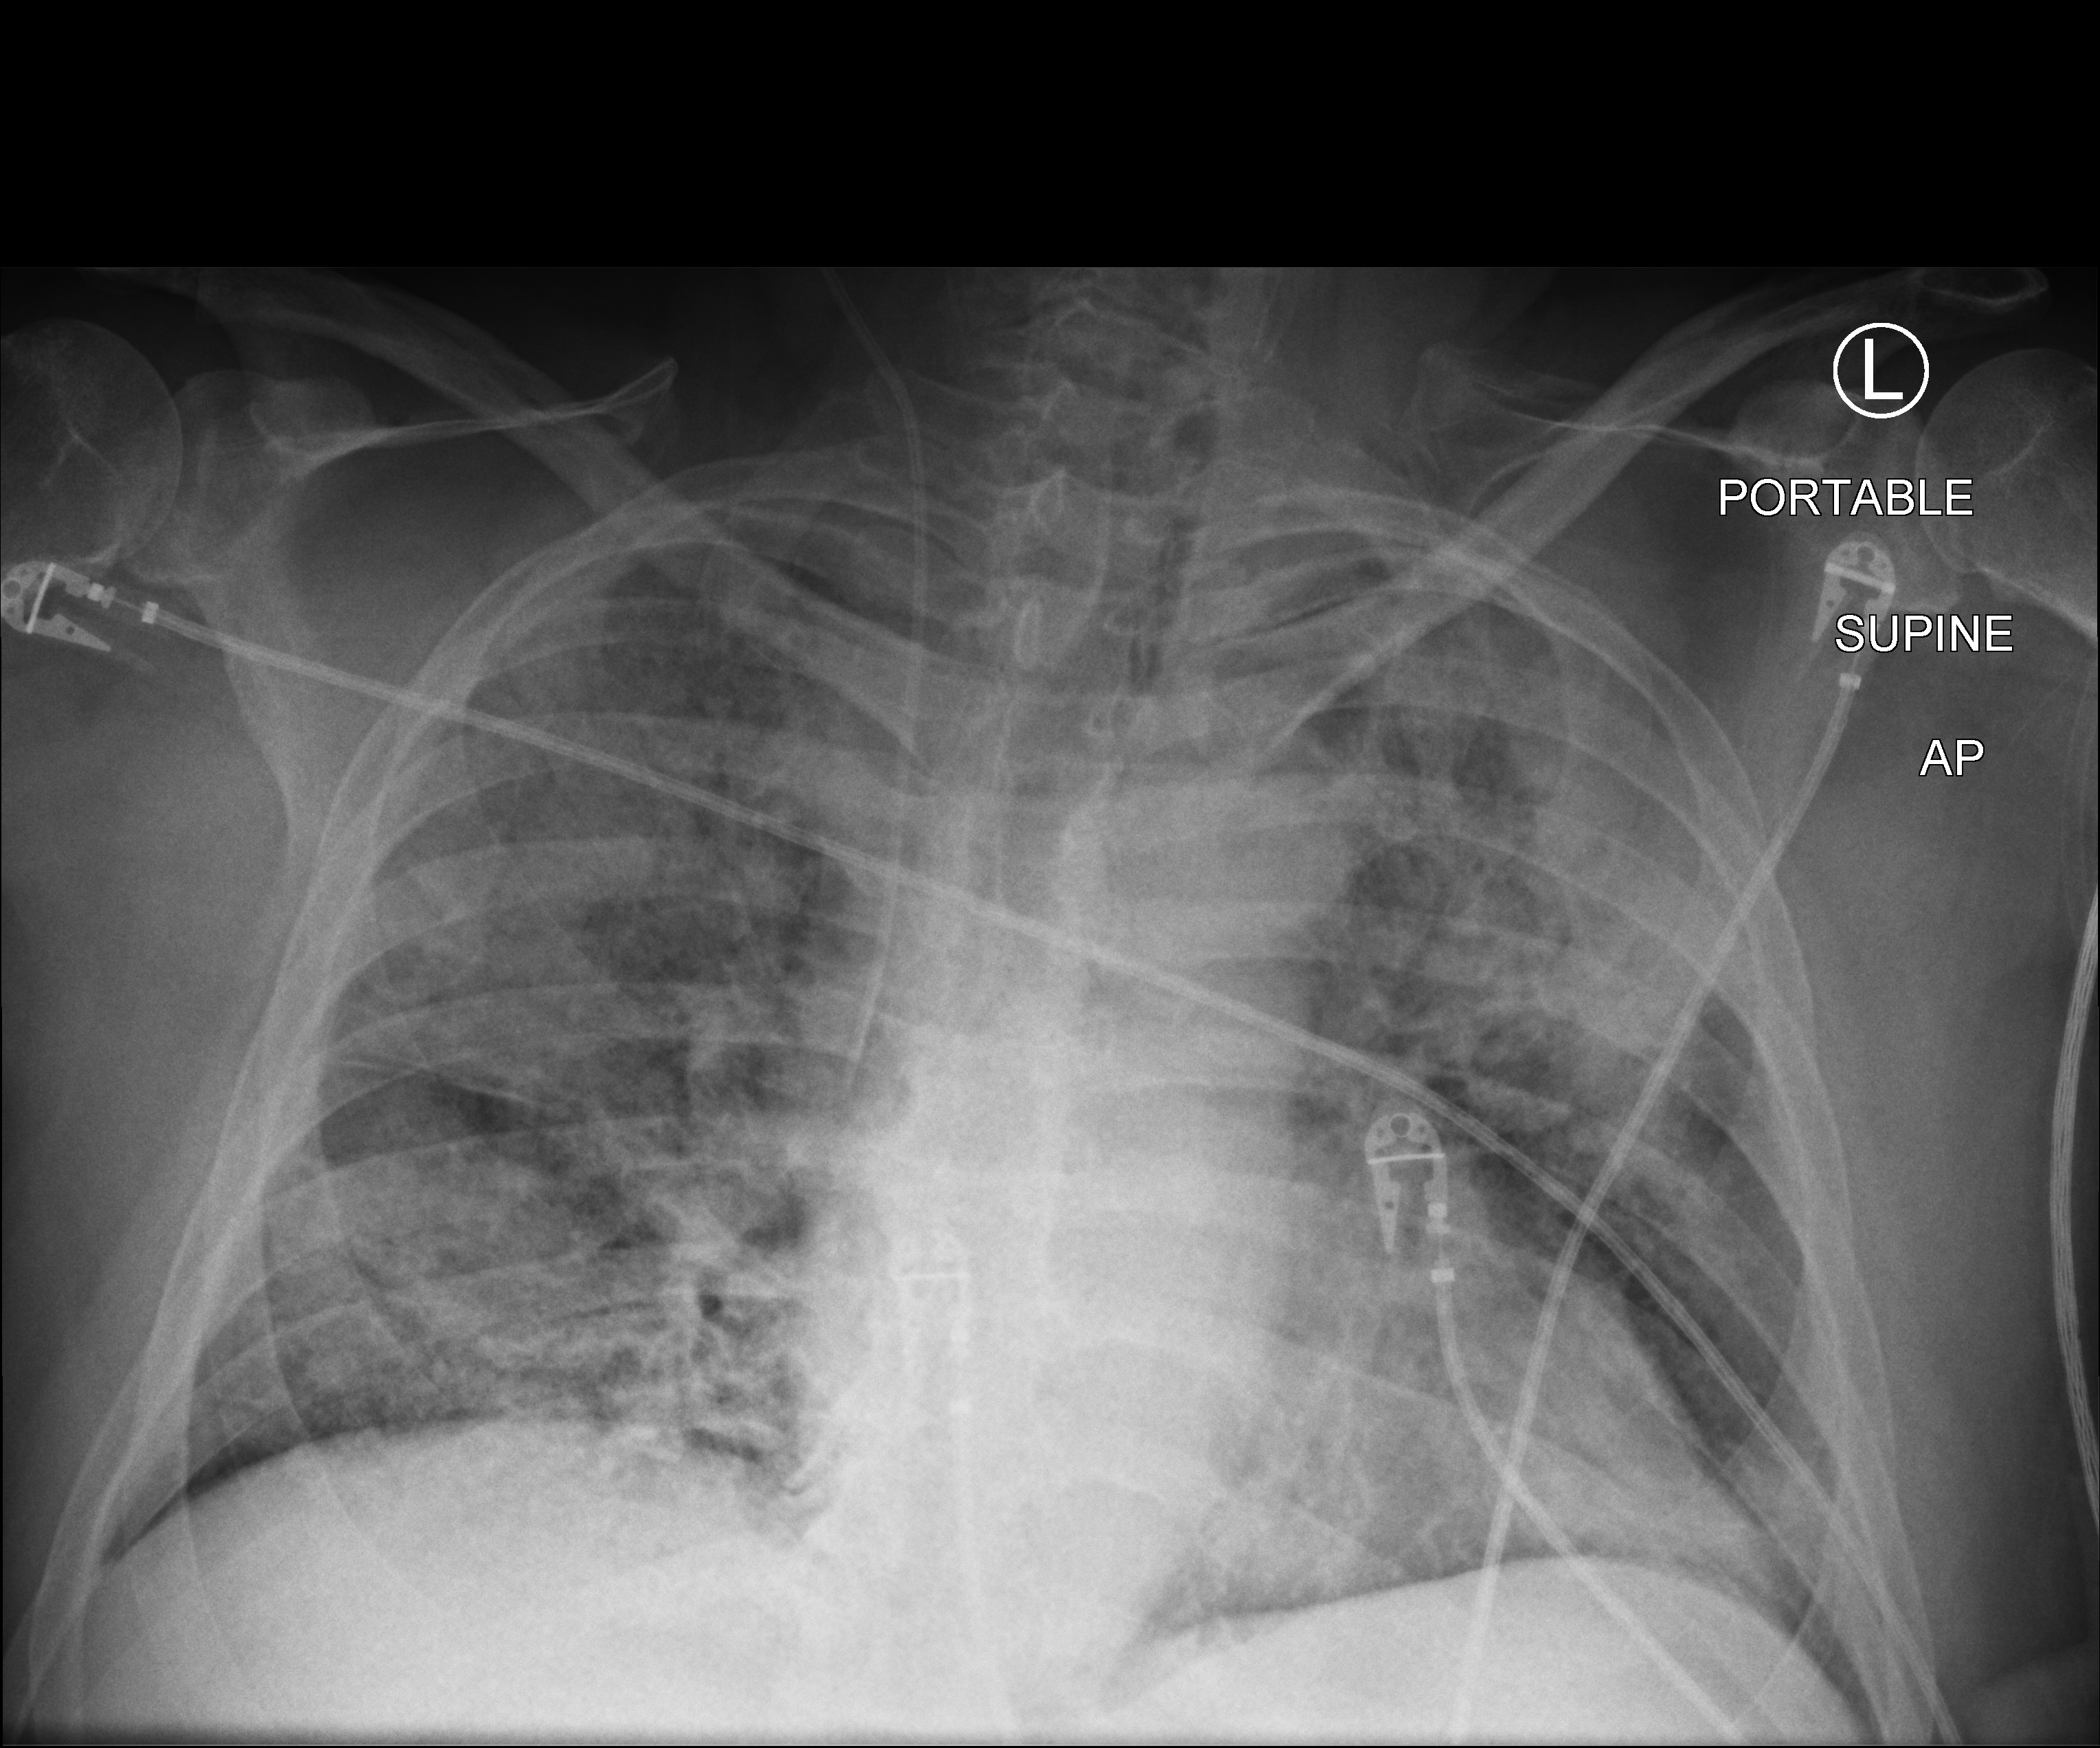
Chest X-ray (portable); anteroposterior (AP) projection. Patient hospitalised with COVID-19; male, aged 60–74 years.
Hospital-stay facts (about this admission, not read from this image; timing relative to this image not recorded):
- diabetes (admission record): no
- COPD (admission record): no